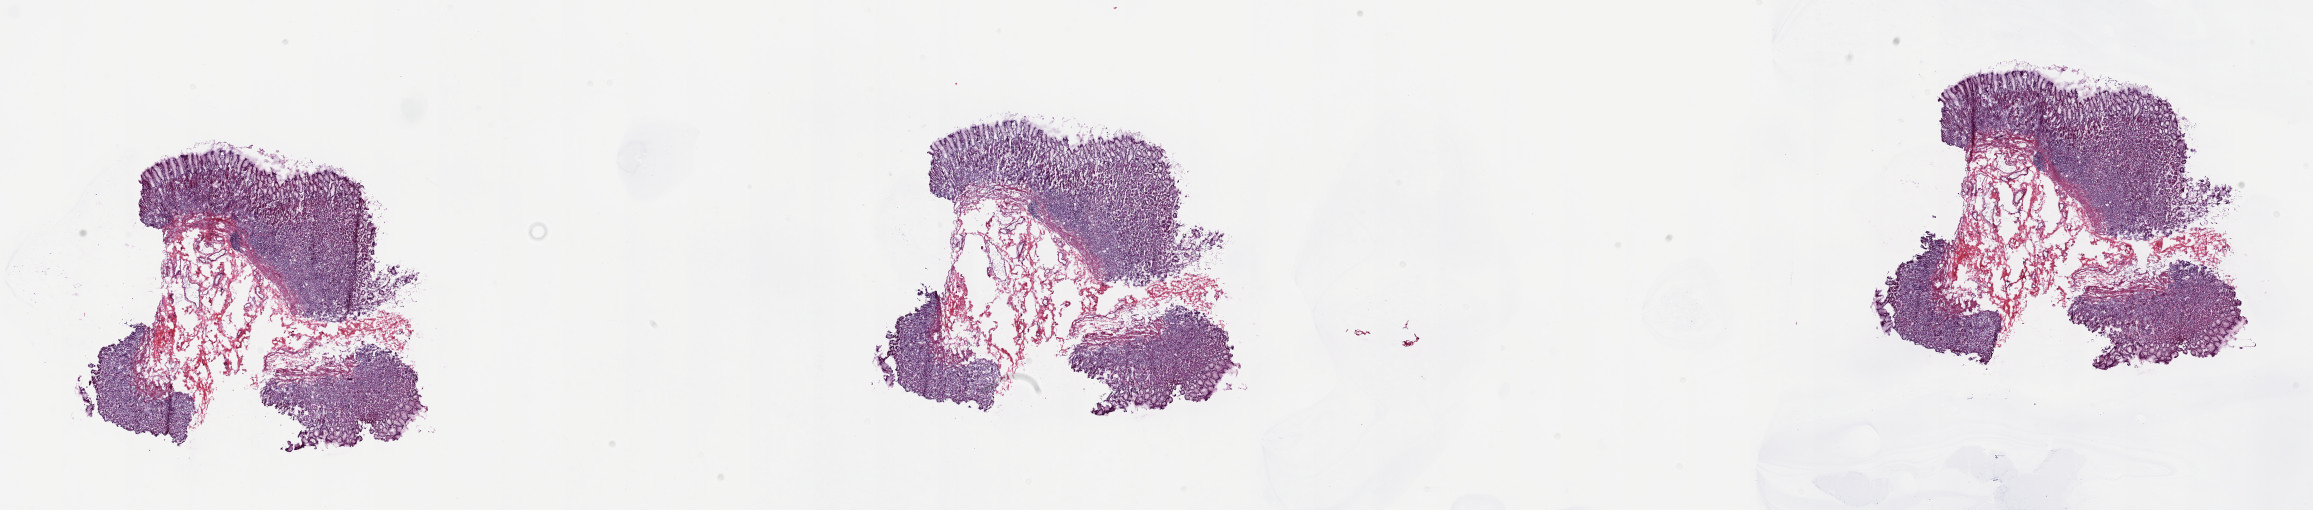
Hematoxylin and eosin (H&E) stained whole-slide image, shown as a low-resolution overview of the whole scanned area (about 36.7 x 8.1 mm, slide scanned at 20x); frozen section from the top of the tissue portion; esophagus, solid tissue normal (non-tumour tissue) sample. Patient: male, age at initial diagnosis 75 years. Slide review estimates, as recorded: tumour cells 0%, tumour nuclei 0%, normal cells 100%, stromal cells 0%, necrosis 0%. Infiltration values recorded for this section: lymphocyte infiltration 4%, monocyte infiltration 0%, neutrophil infiltration 0%.
This section: solid tissue normal (non-tumour) sample from the same patient. Patient diagnosis: Adenocarcinoma, NOS (lower third of esophagus).